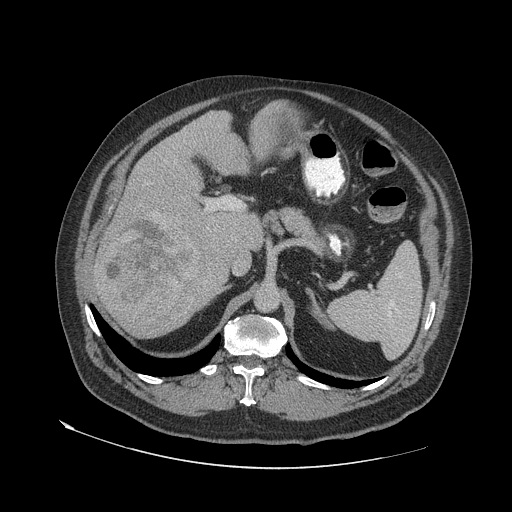
Contrast-enhanced abdominal CT (liver protocol), one axial slice. Slice 38 of 79 in the series (ordered by position). Reconstruction kernel STANDARD. Soft-tissue window (W 400 / L 40 HU). 2.5 mm slice thickness. 512 × 512 image matrix, field of view 480 × 480 mm. From the clinical record (not read from this slice): diagnosis: hepatocellular carcinoma (patient treated with transarterial chemoembolisation; whether this scan precedes or follows treatment is not stated here); TNM stage (as recorded): Stage-IVA; Child-Pugh class: A; tumour differentiation: well differentiated.
Outlined on this slice (semi-automatic segmentation, software-assisted and operator-edited):
- liver parenchyma outside the tumour (the mass and vessels are separate outlines, so this box may not span the whole liver): bounding box (x1, y1, x2, y2) in pixels: (94, 100, 291, 338)
- mass: (95, 216, 202, 316)
- liver vessels: (225, 199, 243, 210)